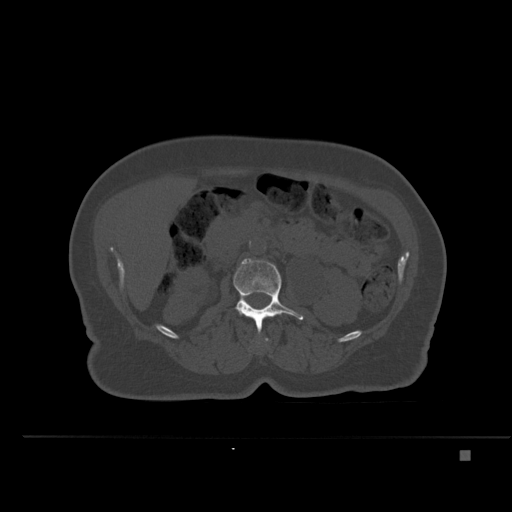
CT including the spine, one axial slice; bone window (W 1800 / L 400 HU); 1.5 mm slice thickness; 512 × 512 image matrix. Patient: female, 74 years. Case-level facts recorded for this patient, not image findings: primary cancer: colon.
Structures marked on this image (semi-automatic segmentation, software-assisted and operator-edited):
- L1 vertebra: bounding box (x1, y1, x2, y2) in pixels: (265, 338, 268, 341)
- L2 vertebra: (234, 259, 304, 332)